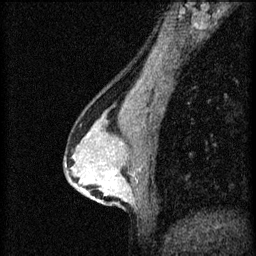
Breast MRI (dynamic contrast-enhanced), one sagittal slice. Position 33 of 60 along the scan axis. 3 images stored at this slice position (order not interpretable as contrast timing). 1.5 T. TE 4.2 ms, TR 8.2 ms. 2 mm slice thickness. 256 × 256 image matrix. Female patient, age 44 years.
Outlined on this slice (semi-automatic segmentation, software-assisted and operator-edited):
- analysis volume of interest (the breast-tissue region the enhancement analysis was run in; not a lesion): box from (x=94, y=162) to (x=137, y=205) px
- tumour enhancement mask (voxels above the 70 % enhancement threshold inside the analysis volume of interest): (x=108, y=172)–(x=117, y=185)